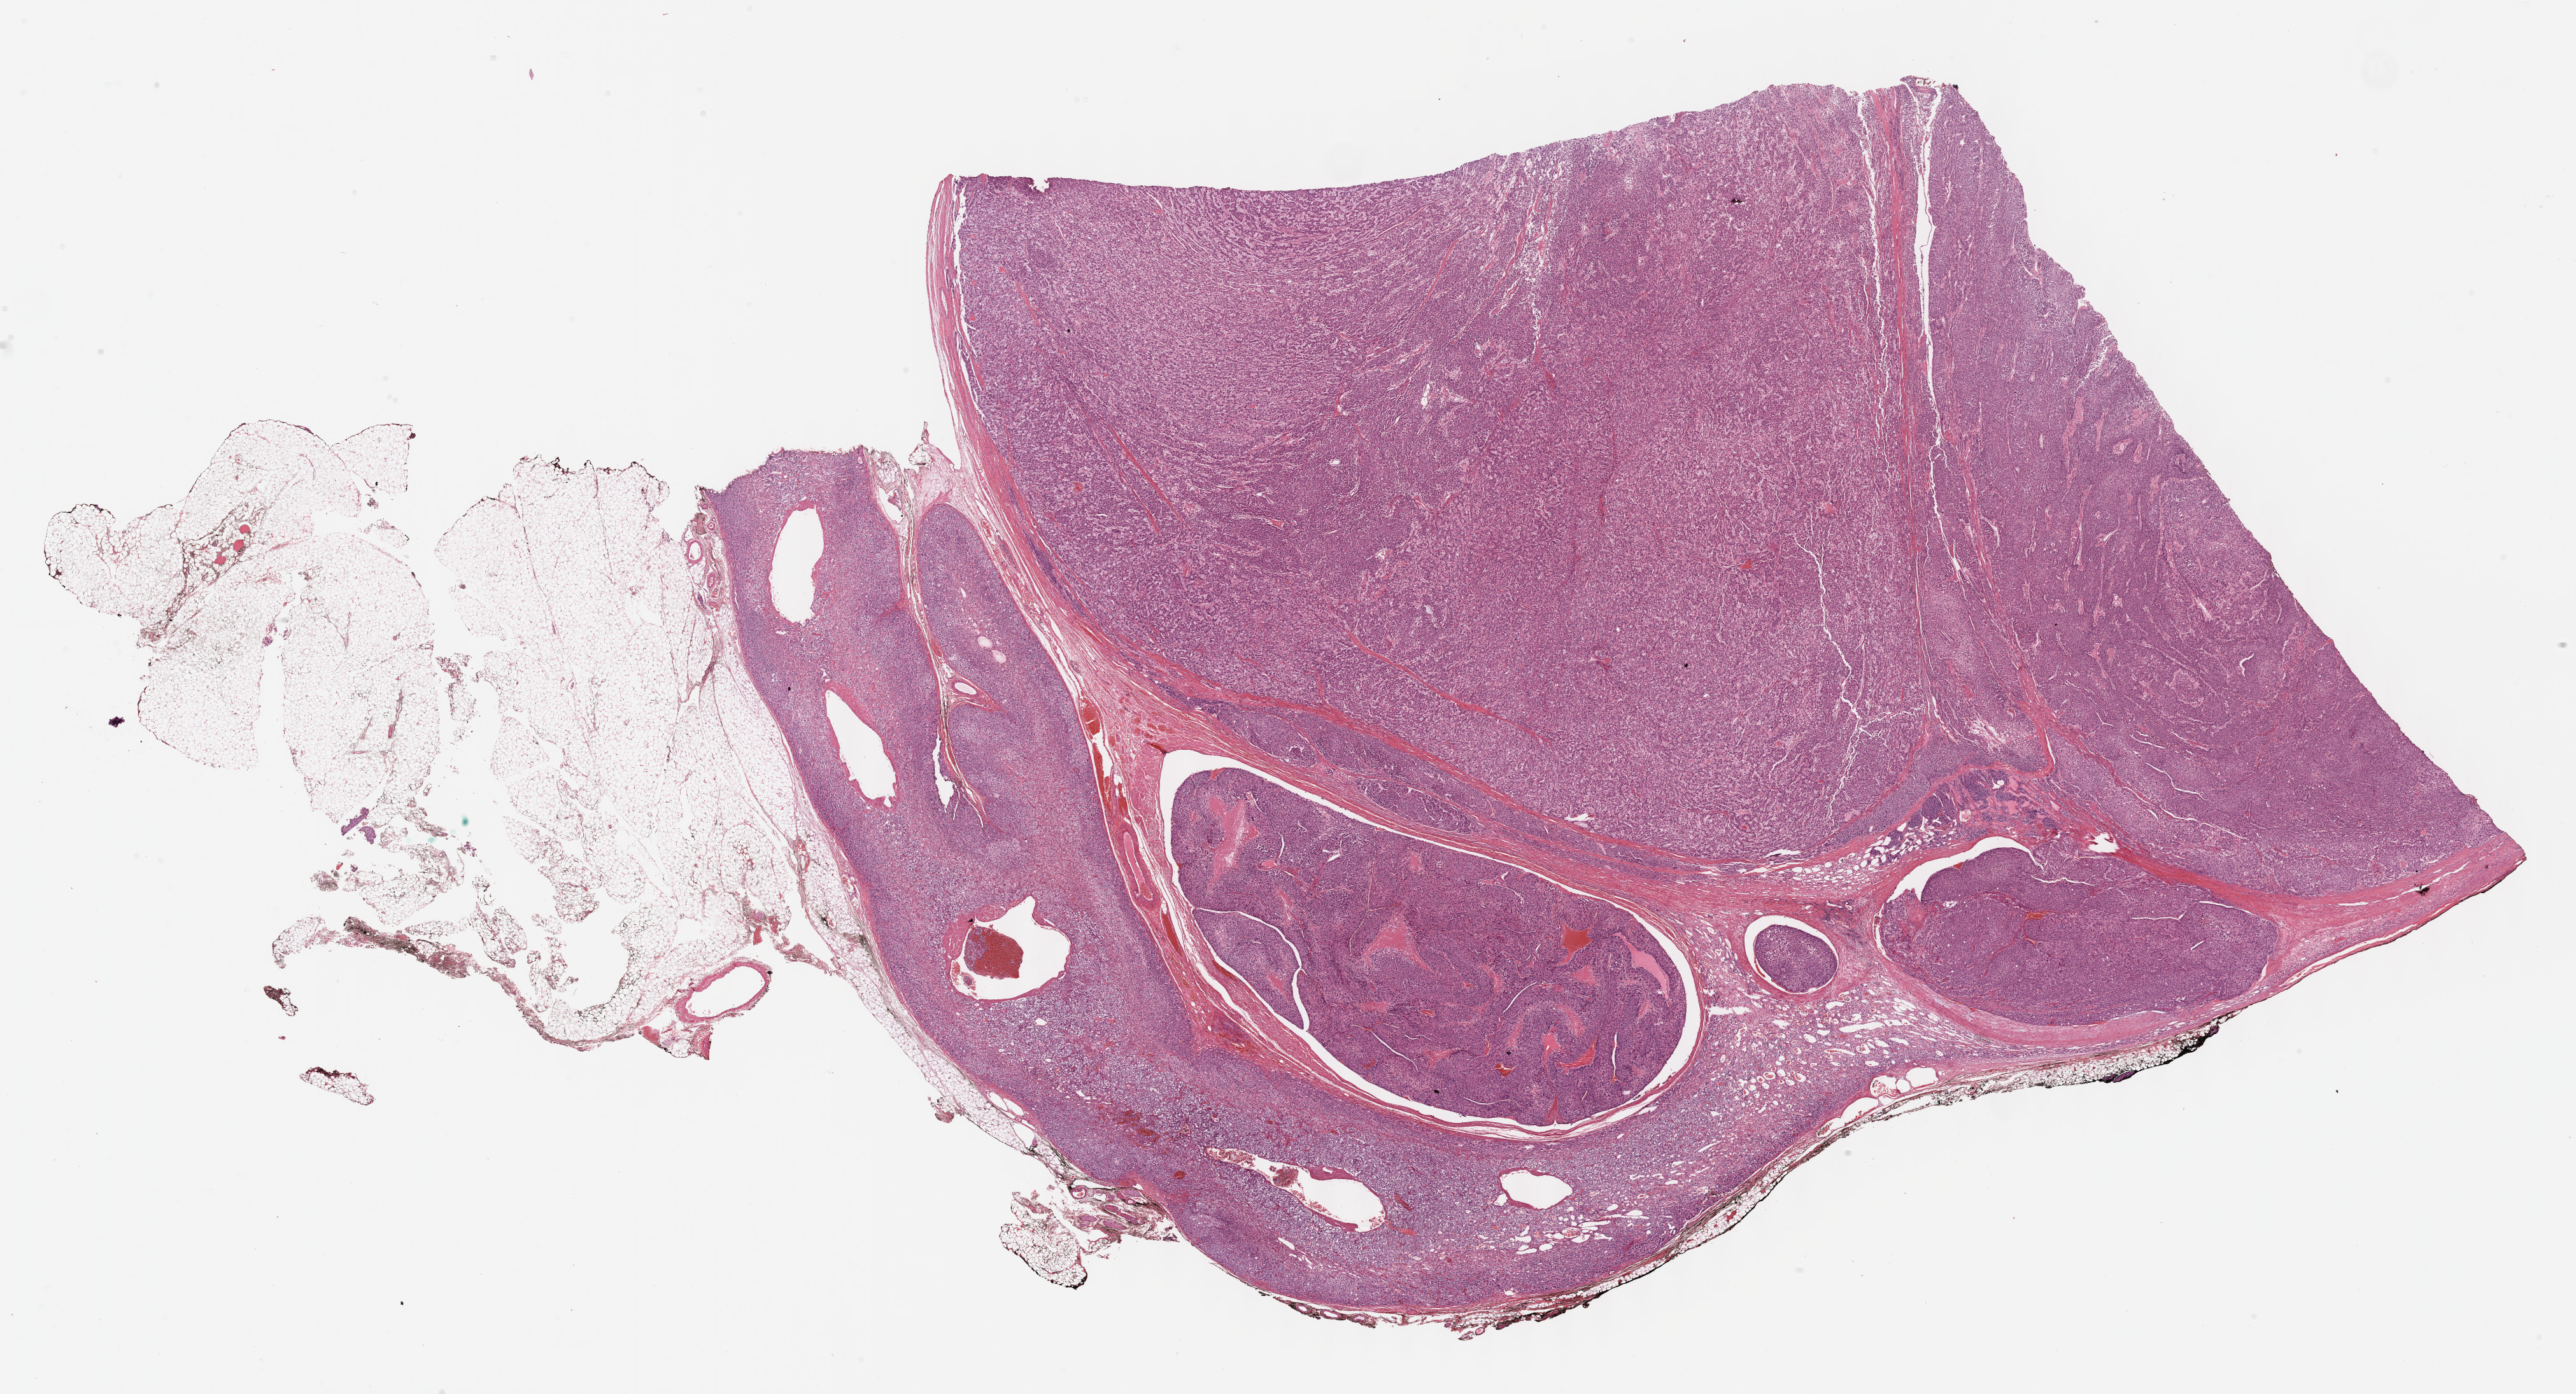
H&E whole-slide image, a low-resolution overview of the entire scanned area, about 32.7 x 17.7 mm (slide scanned at 40x); formalin-fixed paraffin-embedded (FFPE) diagnostic section; adrenal cortex, primary tumour sample. Female, age 25 years at initial diagnosis.
* pathologic diagnosis: Adrenal cortical carcinoma (cortex of adrenal gland)